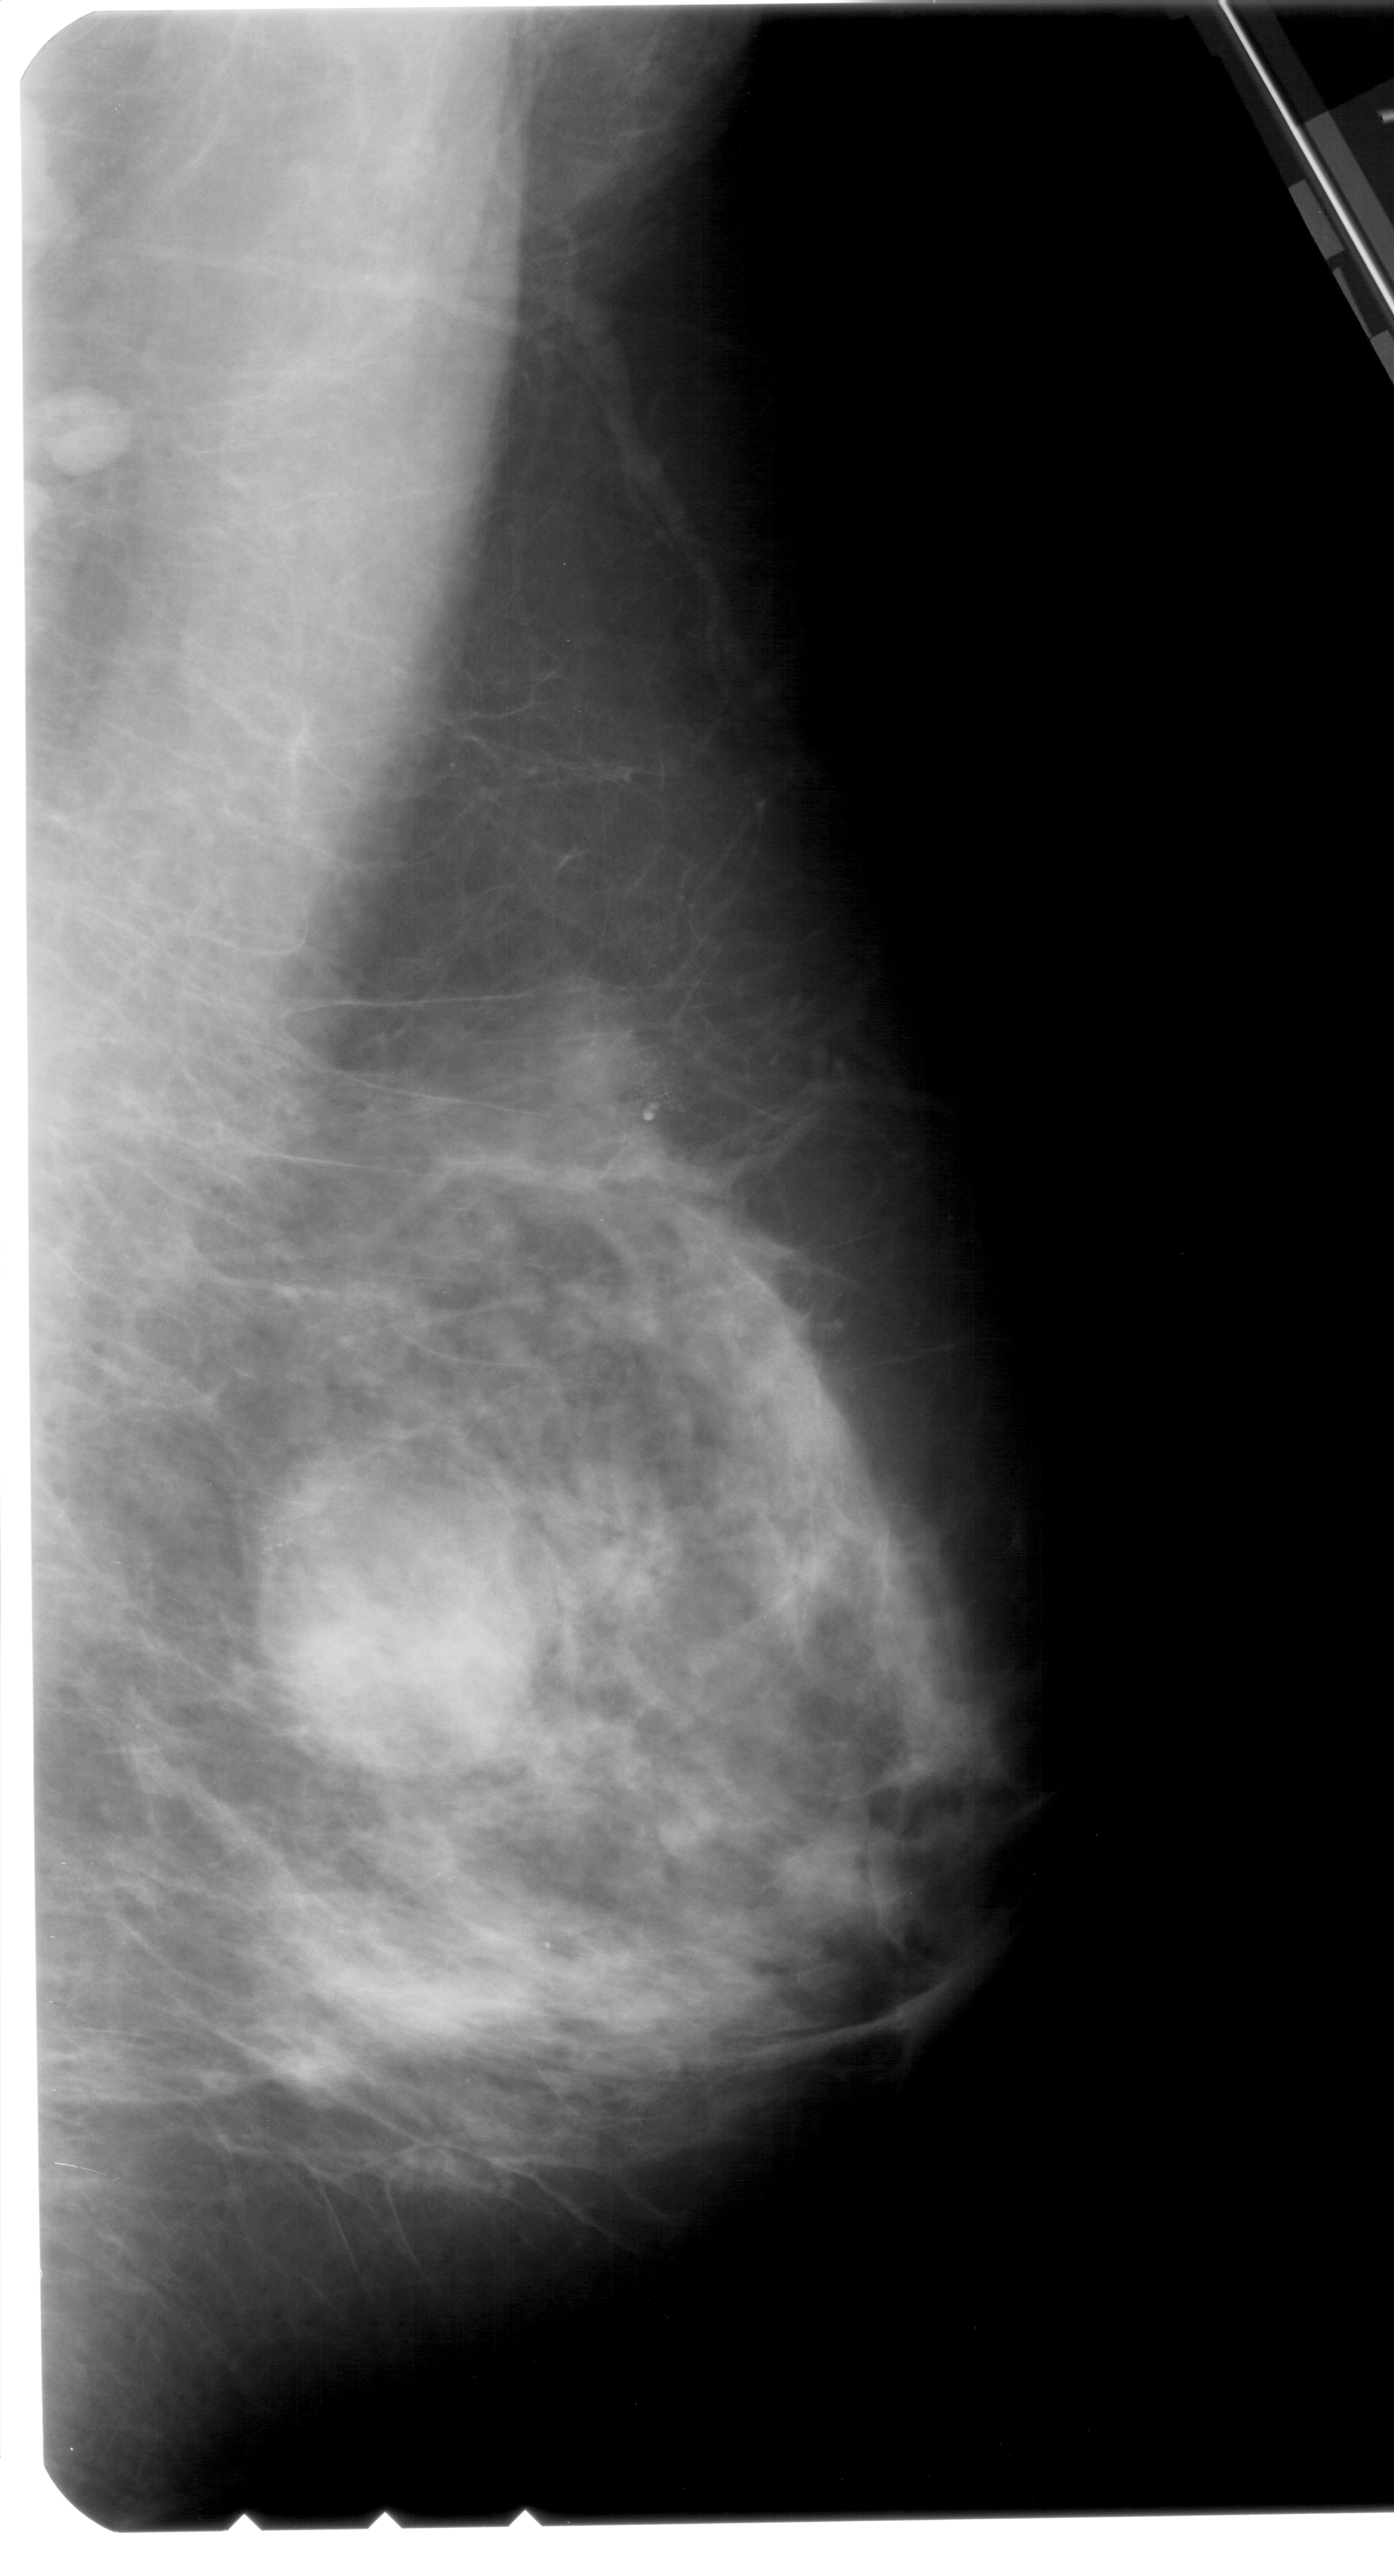
Mammogram (digitized film), right breast, MLO view, breast composition: heterogeneously dense (BI-RADS density category 3 of 4).
Marked findings (only marked abnormalities are described; nothing is implied about the rest of the image): calcifications, morphology pleomorphic, distribution clustered; BI-RADS assessment category 4; subtlety rating 2 on a 1 (subtle) to 5 (obvious) scale; pathology result (as recorded, not read from the image): benign.